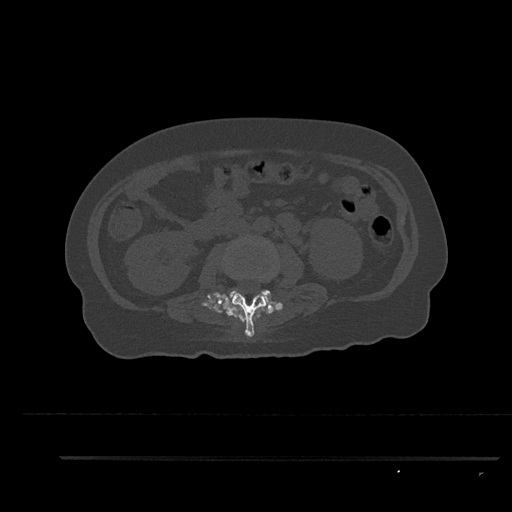
CT including the spine, one axial slice. Position 127 of 797 along the scan axis. Bone window (W 1800 / L 400 HU). 512 × 512 image matrix. Female patient, age 44 years. Case-level facts recorded for this patient, not image findings: primary cancer: renal.
Outlined on this slice (semi-automatically segmented with operator editing):
- L2 vertebra: bounding box (x1, y1, x2, y2) in pixels: (227, 275, 268, 337)
- L3 vertebra: (224, 240, 276, 306)